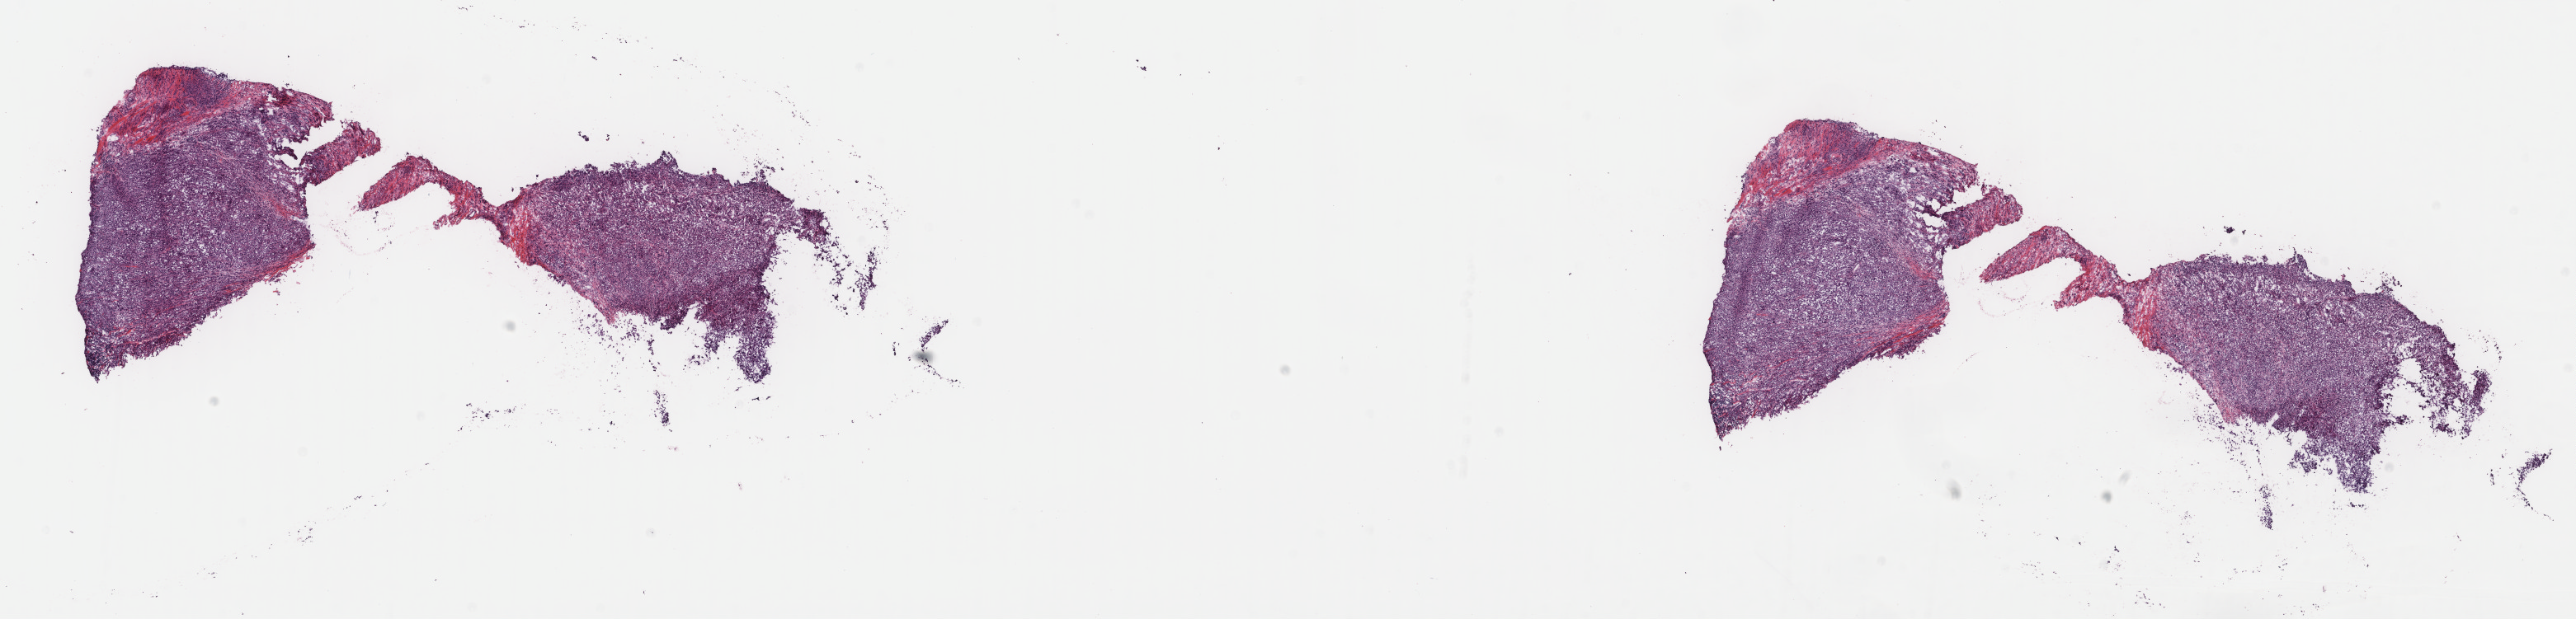
H&E whole-slide image, a low-resolution overview of the entire scanned area, about 24.8 x 6.0 mm. Frozen section from the top of the tissue portion. Metastatic tumour sample, sampled site not recorded. Female patient; age at initial diagnosis 54 years. Pathologist review of this section (percent, as recorded): tumour cells 80%, tumour nuclei 80%.
This section: metastatic tumour tissue. Patient diagnosis: Malignant melanoma, NOS.